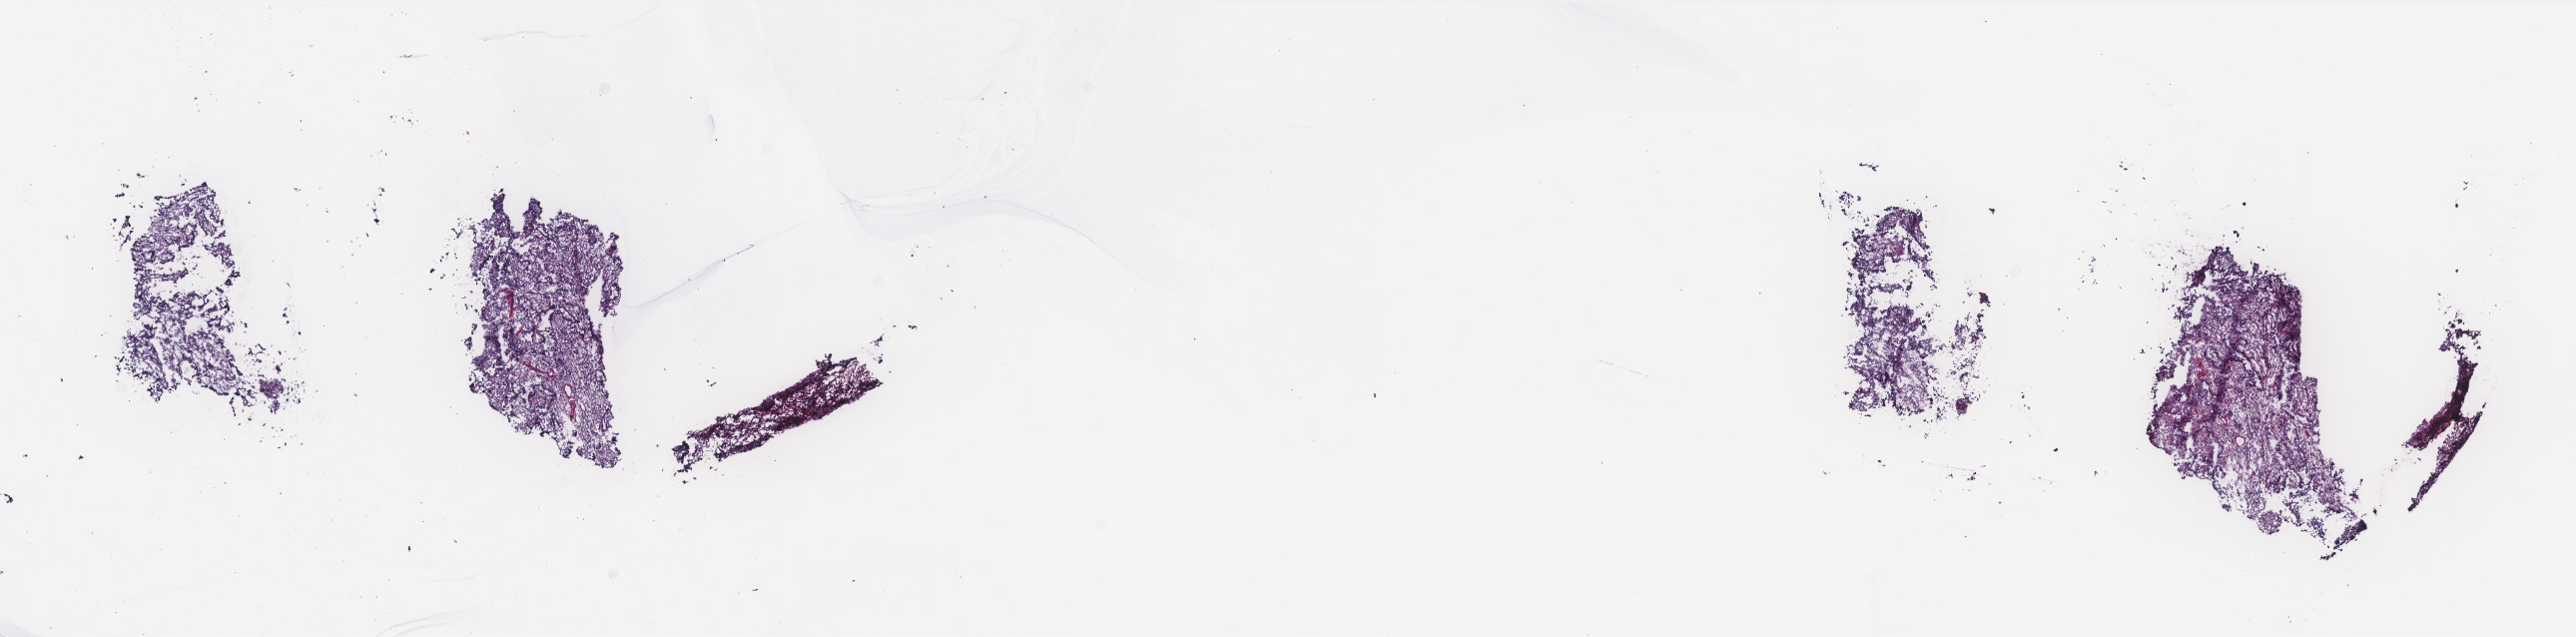
Digitized H&E-stained tissue section (whole slide) — a low-resolution overview of the entire scanned area, about 20.7 x 5.1 mm. Frozen section from the top of the tissue portion. Sample: primary tumour, uterus. Female, age 79 years at initial diagnosis. Histologic grade: G3 (poorly differentiated). Composition of this section per pathologist review: tumour cells 85%, tumour nuclei 85%, normal cells 0%, stromal cells 15%, necrosis 0%. Inflammatory infiltration, as recorded: lymphocyte infiltration 8%, monocyte infiltration 3%, neutrophil infiltration 3%.
• histologic diagnosis: Serous cystadenocarcinoma, NOS (endometrium)
• FIGO stage: IVB